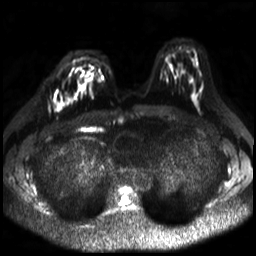
Breast MRI, one axial slice; slice 15 of 30 in the series (ordered by position); diffusion-weighted series; image 2 of 4 stored at this slice position (different b-values; order by instance number); 3 T; 4 mm slice thickness; 256 × 256 image matrix, field of view 320 × 320 mm. Female patient.
Annotated regions visible in this slice (expert manual segmentation):
- tumour on diffusion-weighted imaging: bounding box <53,101,63,112> (left, top, right, bottom; pixels)